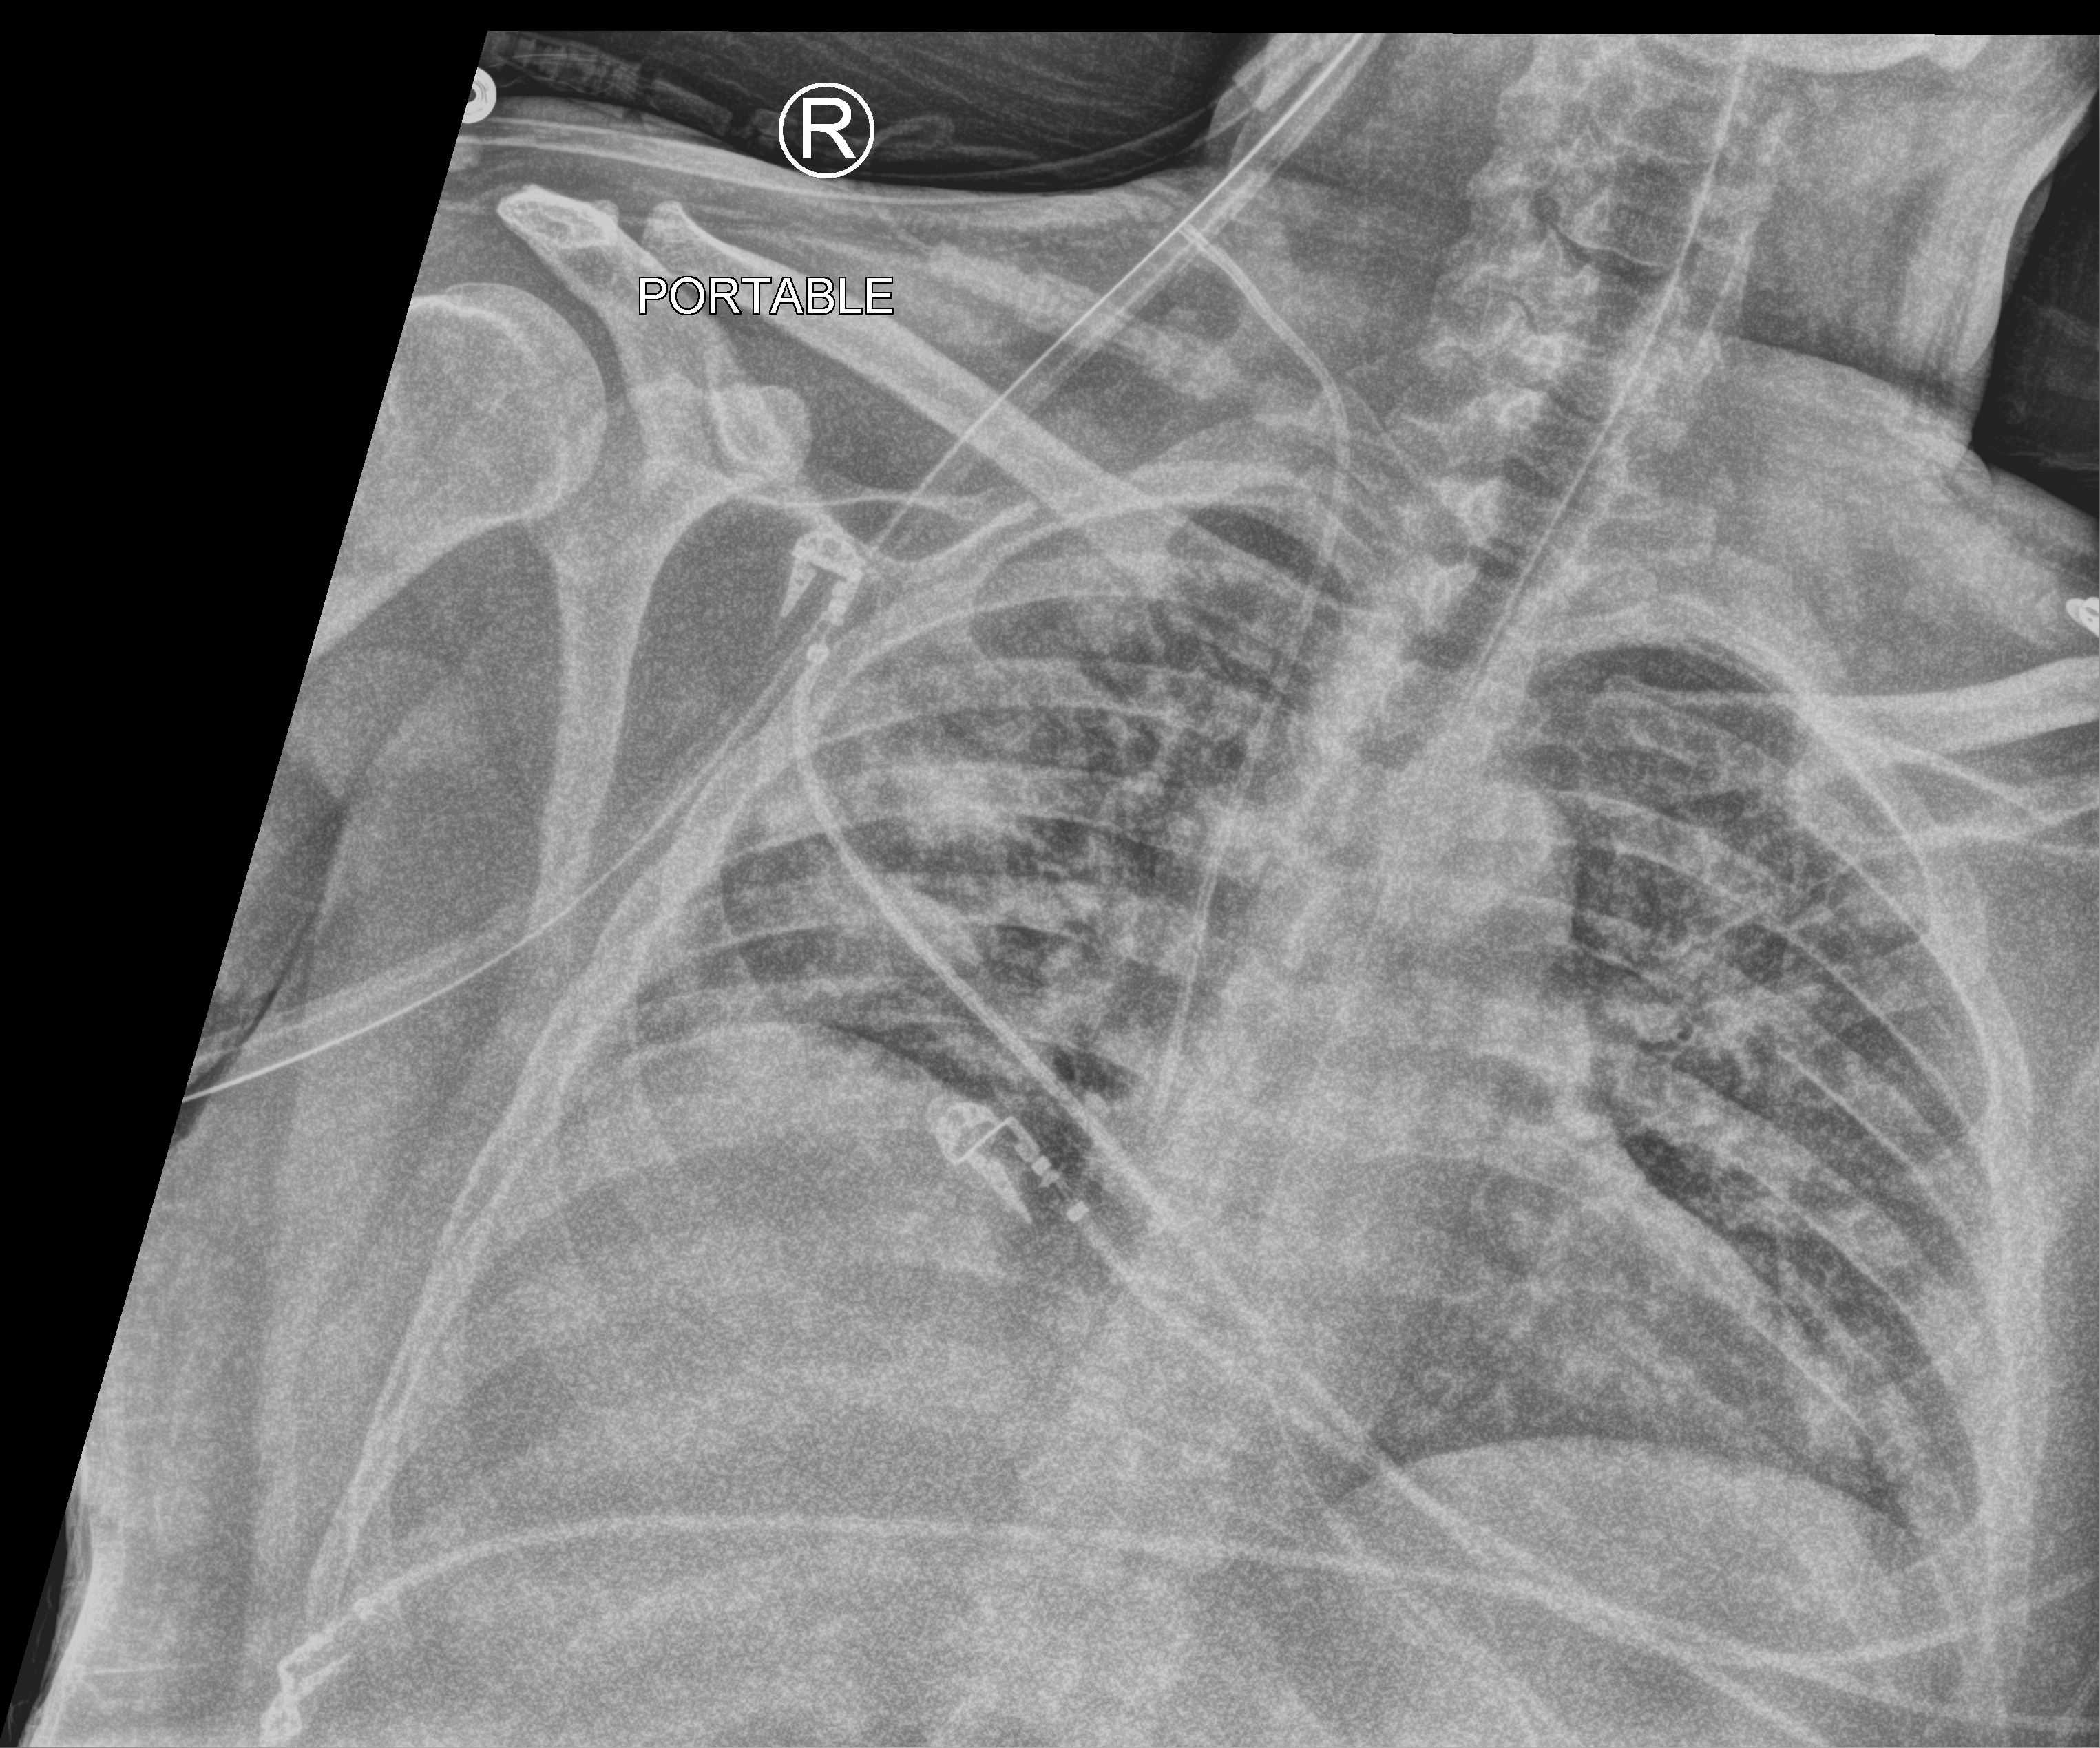
Bedside chest radiograph (computed radiography), anteroposterior (AP) projection. Patient hospitalised with COVID-19; male, aged 18–59 years.
Hospital-stay facts (about this admission, not read from this image; timing relative to this image not recorded): COPD (admission record): no.